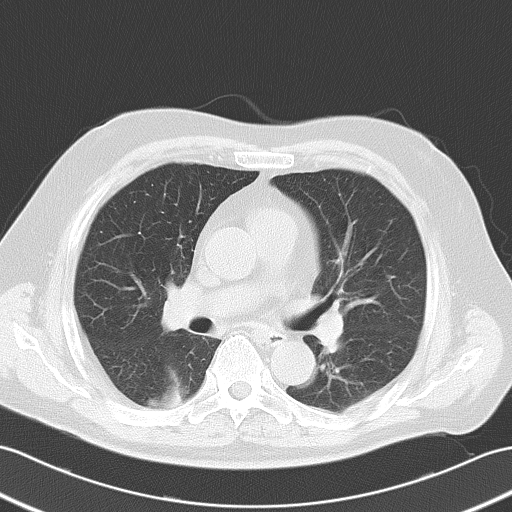
Chest CT, one axial slice; reconstruction kernel B70f; 120 kVp; lung window (W 1500 / L -600 HU); 5 mm slice thickness; 512 × 512 image matrix. Male patient, age 70 years. Case-level facts recorded for this patient, not image findings: clinical TNM (as recorded): T2 N0 M0; histopathological grade: G2.
Annotated regions visible in this slice (rectangle marked by the reading radiologist):
- lung tumour (recorded histology: adenocarcinoma): bounding box (x1, y1, x2, y2) in pixels: (148, 366, 184, 418)